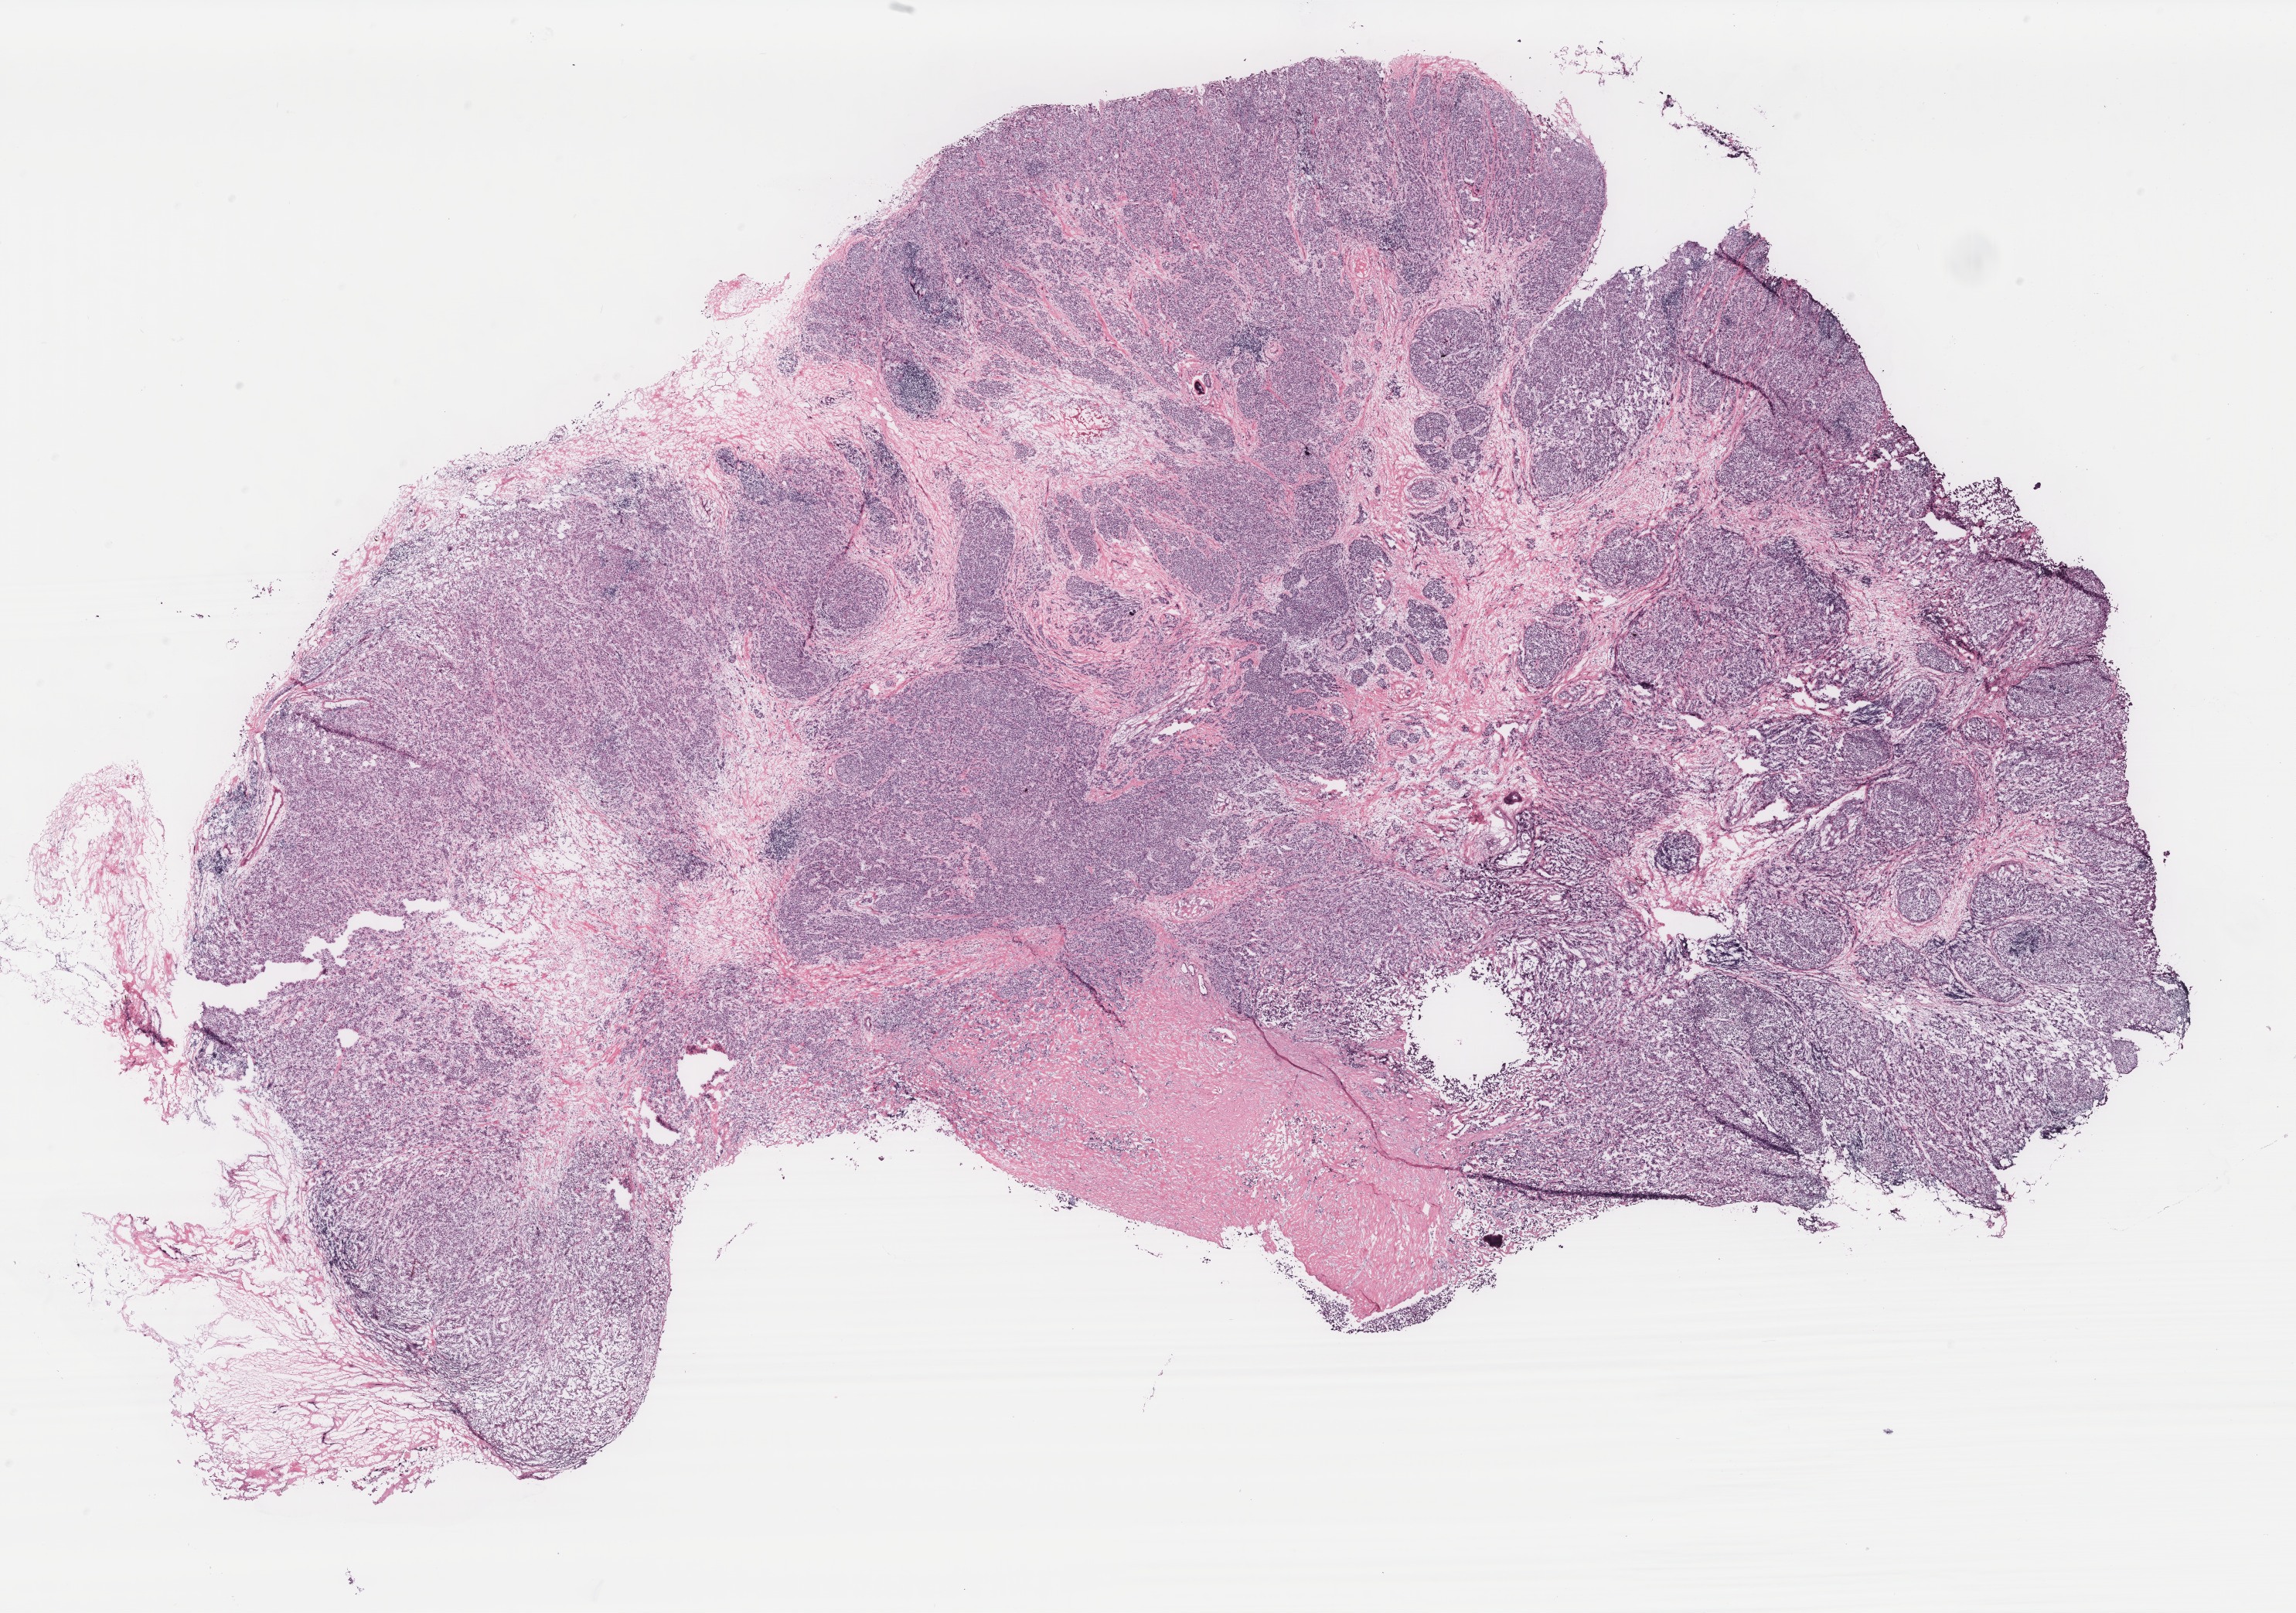
Whole-slide histology image, H&E, whole scanned area (about 23.8 x 16.7 mm, slide scanned at 40x) shown as a low-resolution overview. Breast, tissue type not recorded. Female, 65 y/o.
• patient diagnosis: Infiltrating lobular carcinoma, NOS